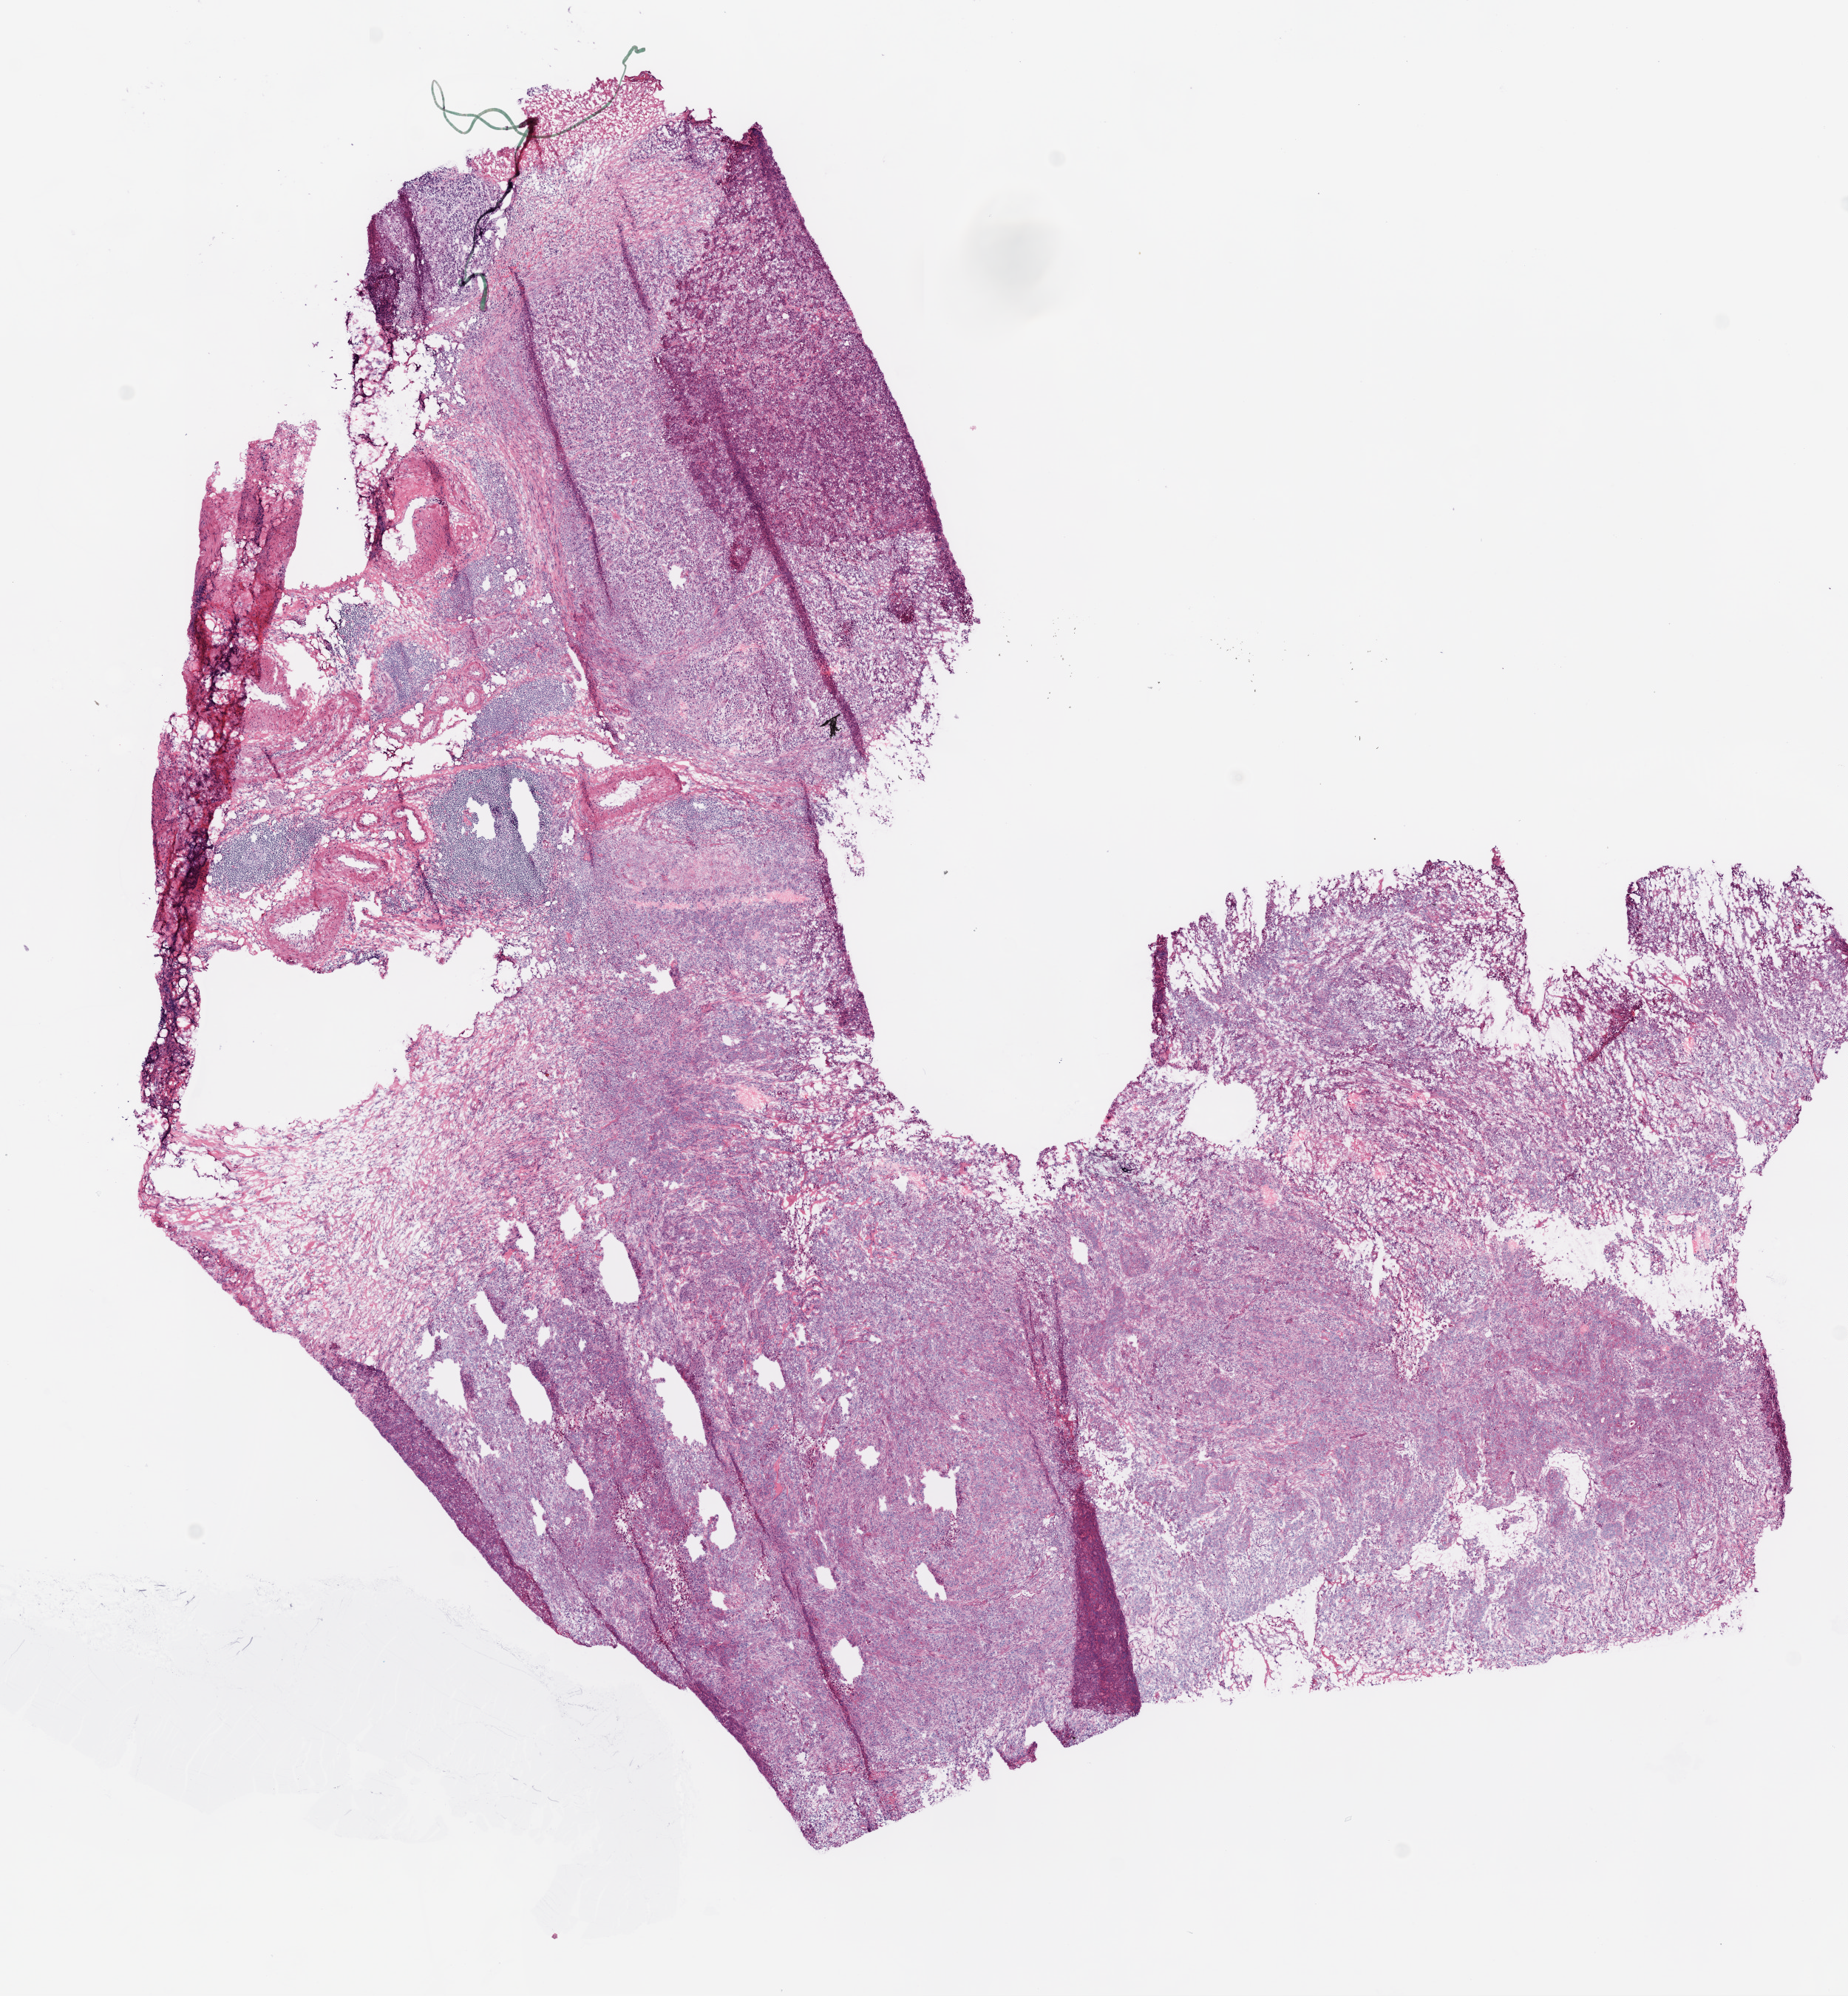
Whole-slide histology image, H&E-stained — low-resolution overview of the scanned area, about 10.0 x 10.8 mm (acquisition: 20x scan). Frozen section from the top of the tissue portion. Colon, primary tumour sample. Male patient; age at initial diagnosis 77 years. Pathologist review of this section (percent, as recorded): tumour cells 80%, tumour nuclei 75%, normal cells 19%, necrosis 1%. Inflammatory infiltration, as recorded: lymphocyte infiltration 5%.
* pathologic diagnosis: Adenosquamous carcinoma (ascending colon)
* AJCC pathologic stage: II
* TNM: T3 N0 M0